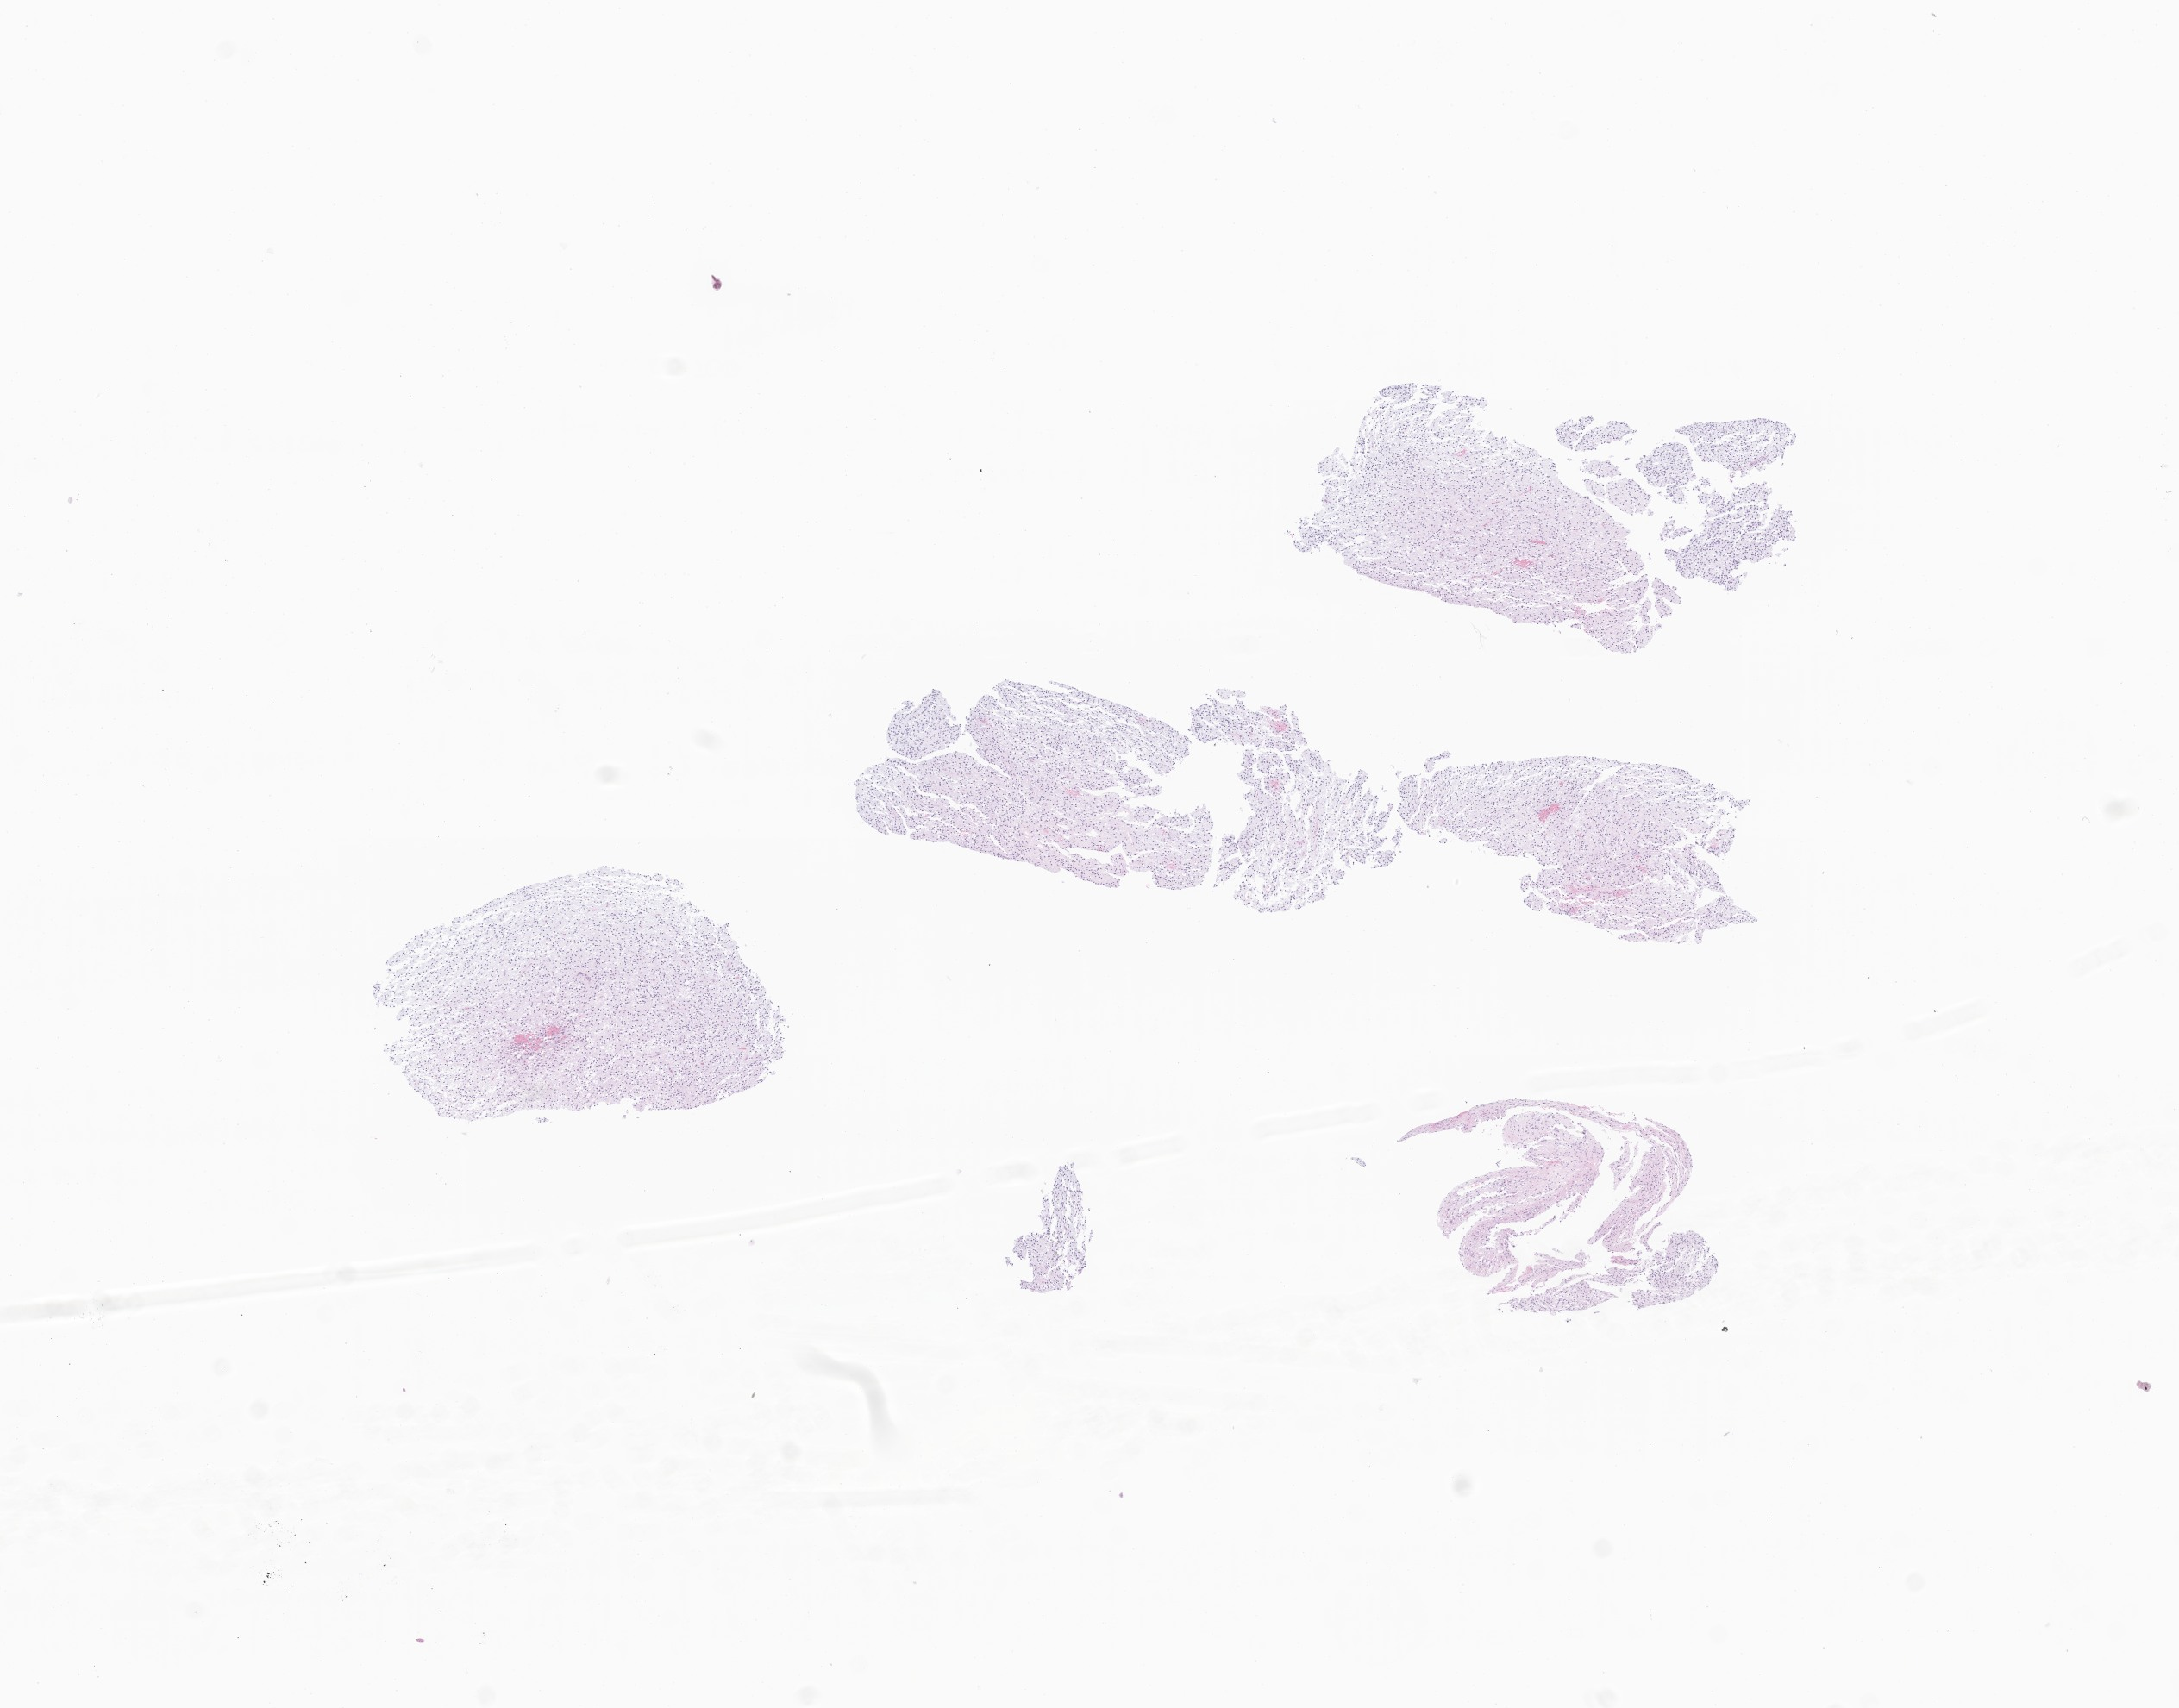
Hematoxylin and eosin (H&E) whole-slide image of tumor tissue from the brain — whole scanned area (about 10.7 x 8.4 mm) shown as a low-resolution overview; FFPE section. Male patient, age 78 months (6 years 6 months).
Recorded diagnosis: Dysembryoplastic neuroepithelial tumor.